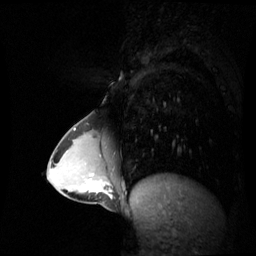
Breast MRI (dynamic contrast-enhanced), one sagittal slice; position 25 of 60 along the scan axis; dynamic contrast-enhanced series, image 2 of 3 at this slice position (ordered by acquisition); 1.5 T; TE 4.2 ms, TR 8.9 ms; 2.4 mm slice thickness; 256 × 256 image matrix. Patient: female, 34 years. From the clinical record (not read from this slice): setting: breast cancer imaged before/during neoadjuvant chemotherapy; receptor status: triple-negative.
Outlined on this slice (semi-automatically segmented with operator editing):
- analysis volume of interest (the breast-tissue region the enhancement analysis was run in; not a lesion): bounding box [x1, y1, x2, y2] px = [65, 168, 112, 204]
- tumour enhancement mask (voxels above the 70 % enhancement threshold inside the analysis volume of interest): [90, 186, 100, 193]